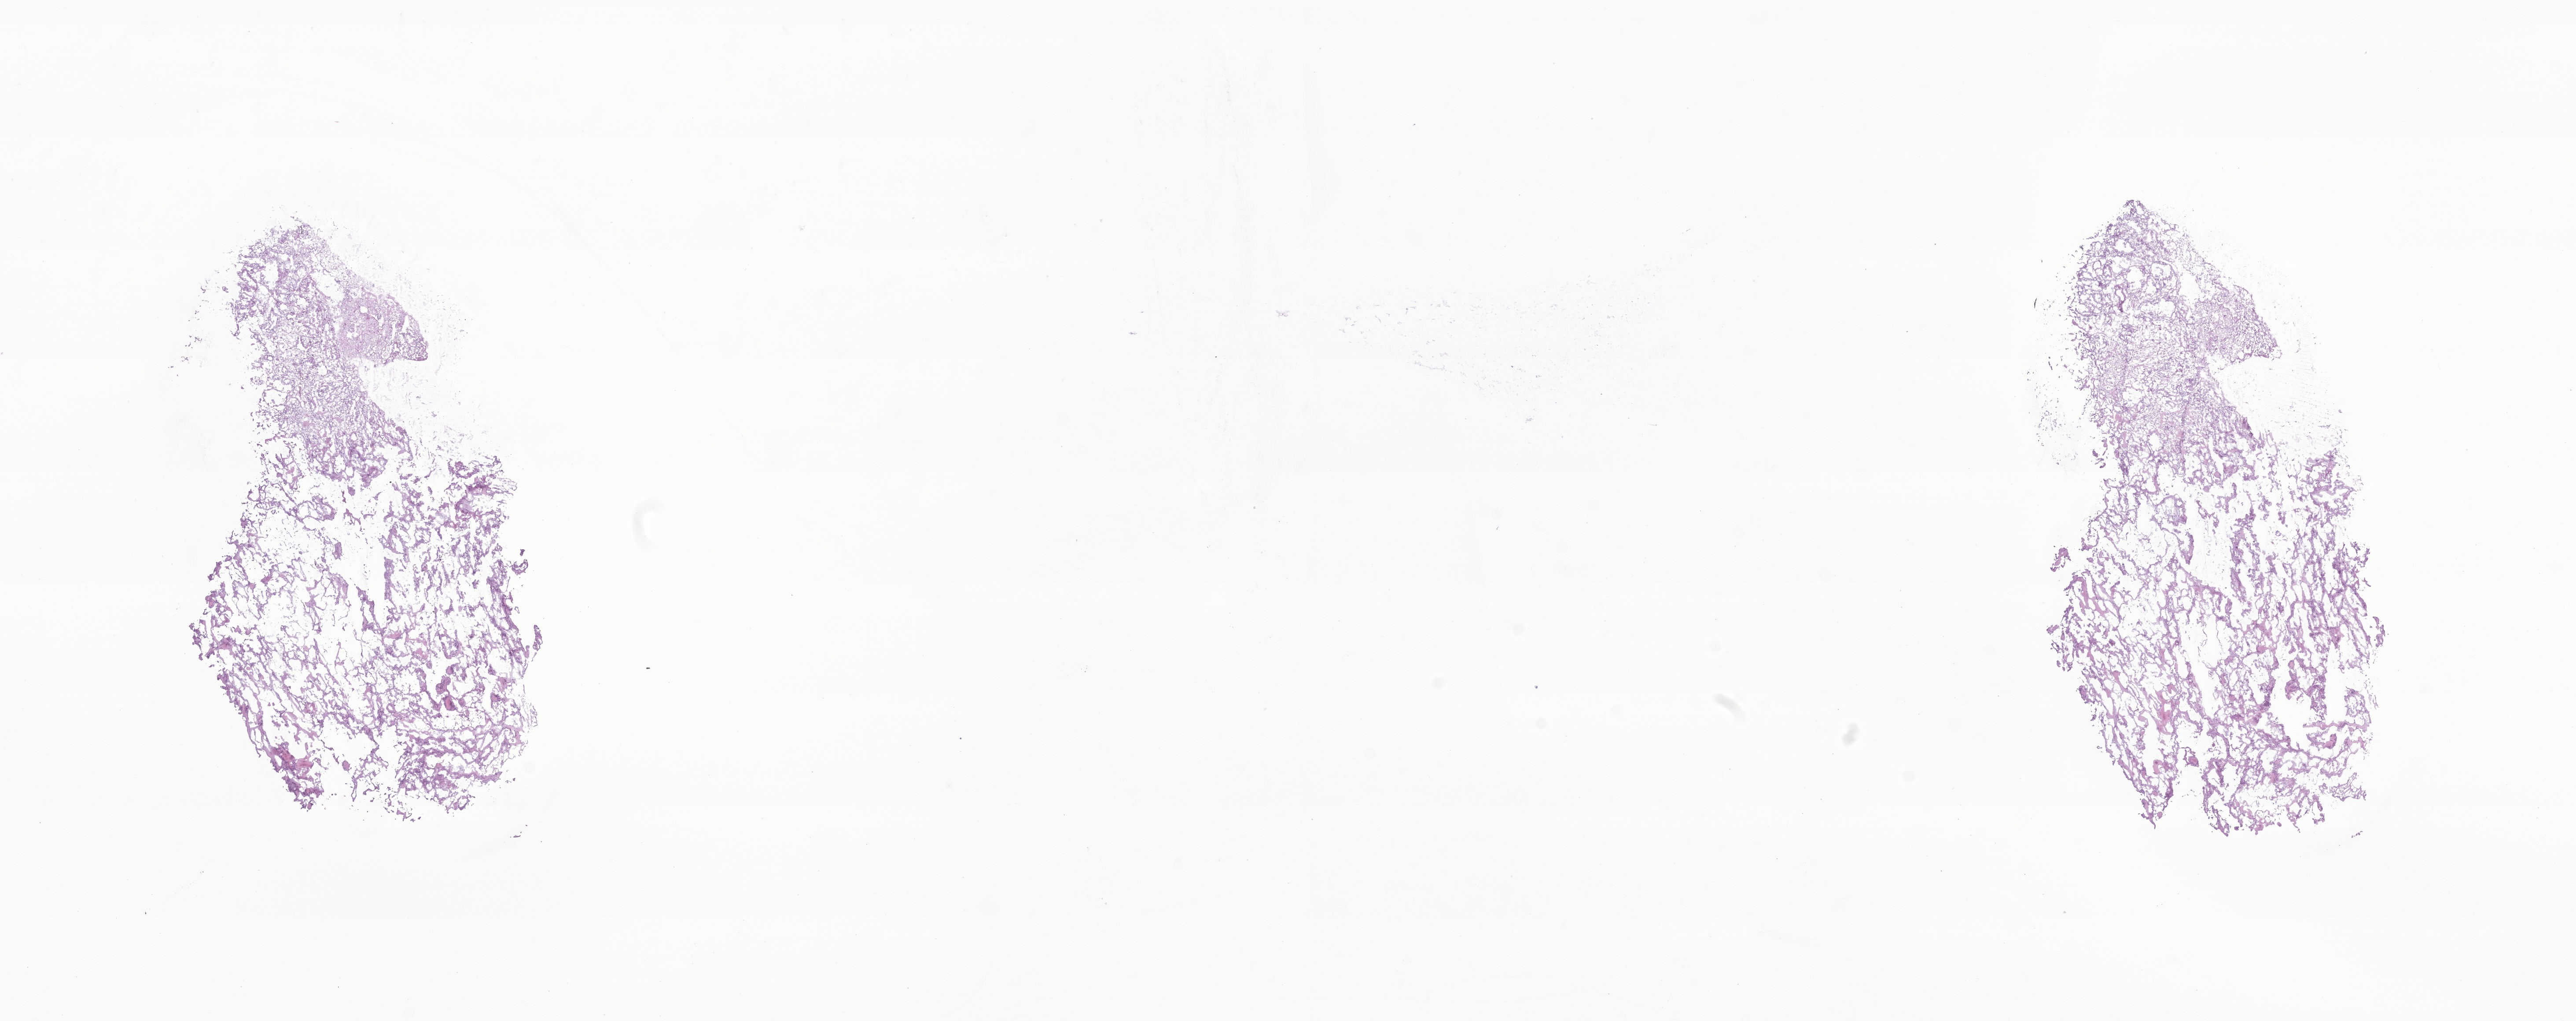
Whole-slide image, hematoxylin and eosin (H&E) stain of tumor tissue from the brain — whole scanned area (about 24.7 x 9.8 mm) shown as a low-resolution overview, cryosection (OCT / tissue freezing medium). Patient: male, age 212 months (17 years 8 months).
Diagnosis (ICD-O-3 morphology term): Hemangioblastoma.